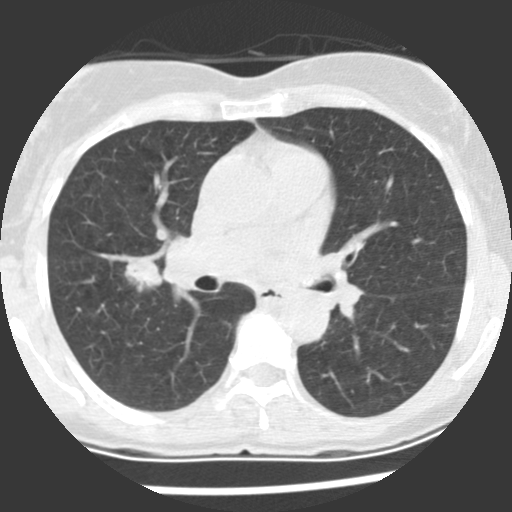
Low-dose screening chest CT, one axial slice. Reconstruction kernel STANDARD. Lung window (W 1500 / L -600 HU). 512 × 512 image matrix, field of view 270 × 270 mm.
Outlined on this slice (outlined manually by an expert reader):
- lesion 1 (tumor, upper lobe of right lung): box from (x=125, y=258) to (x=162, y=292) px